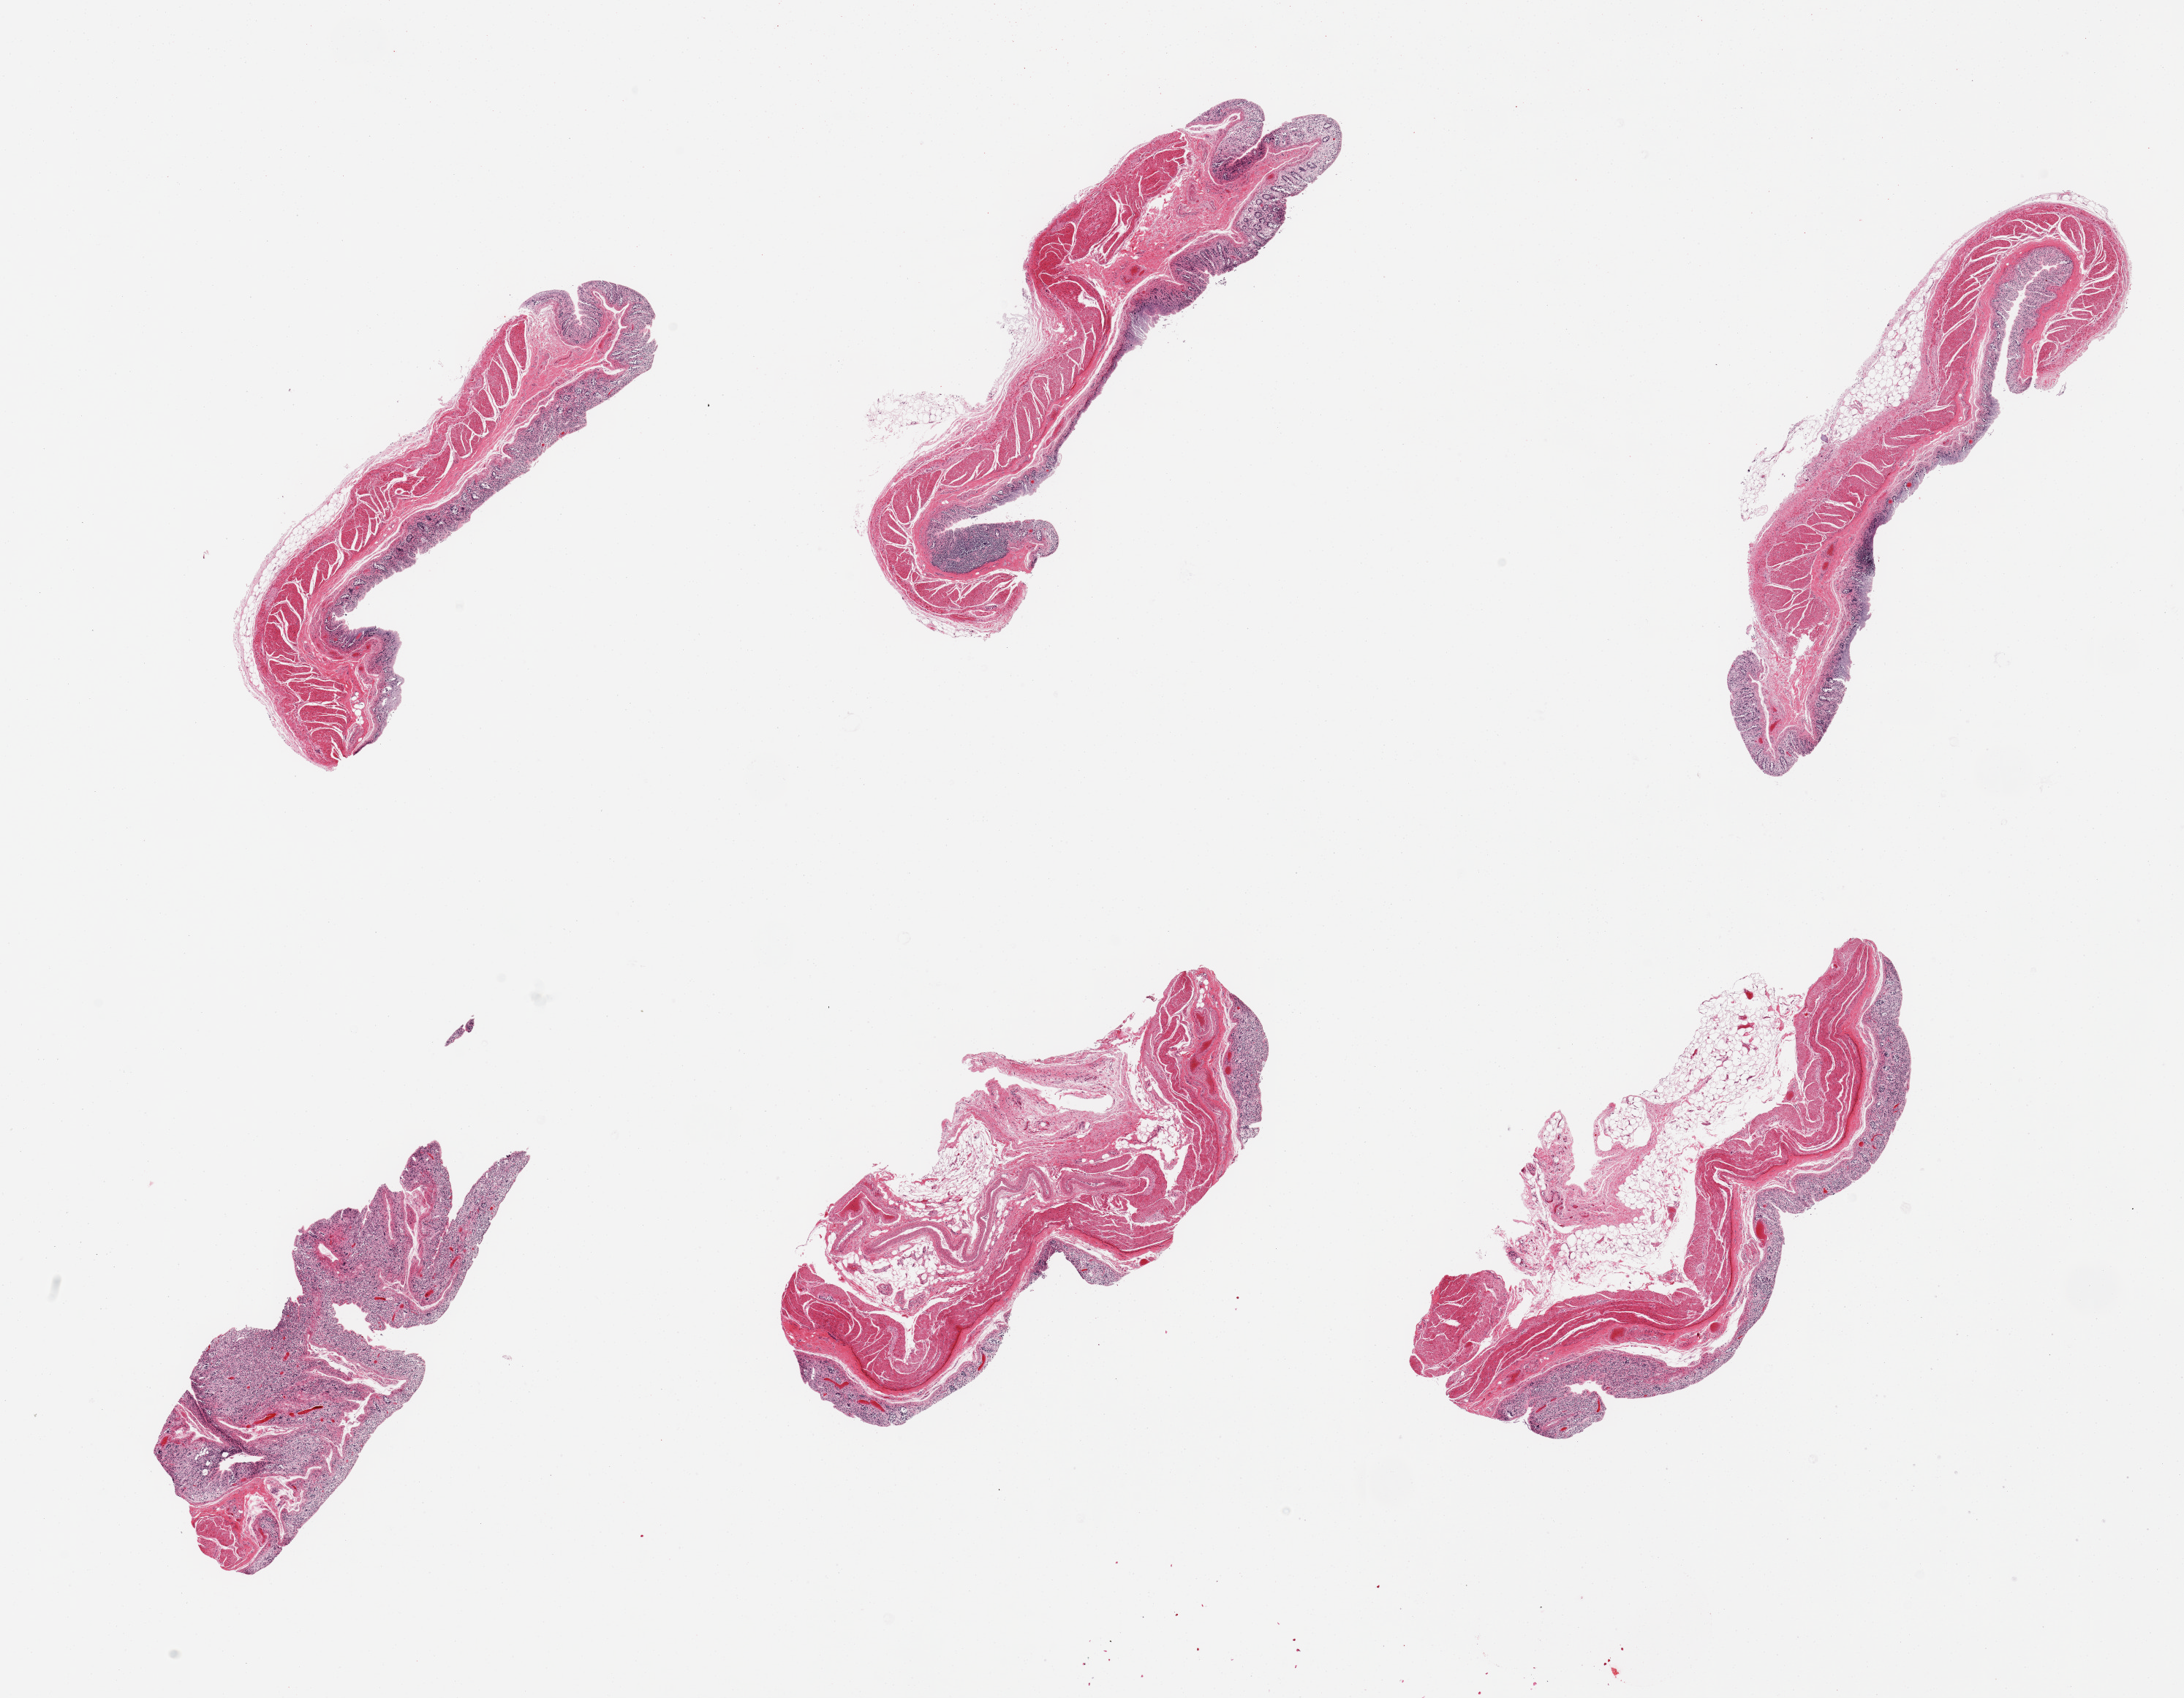
Haematoxylin and eosin whole-slide image — low-resolution overview of the scanned area, about 23.6 x 18.4 mm; PAXgene-fixed paraffin-embedded (PFPE) section; section of transverse colon (target tissue); tissue donor sample. Donor sex: male.
Reviewer comment on this tissue sample: 6 pieces; mucosa largely autolyzed; muscle in somewhat better shape.